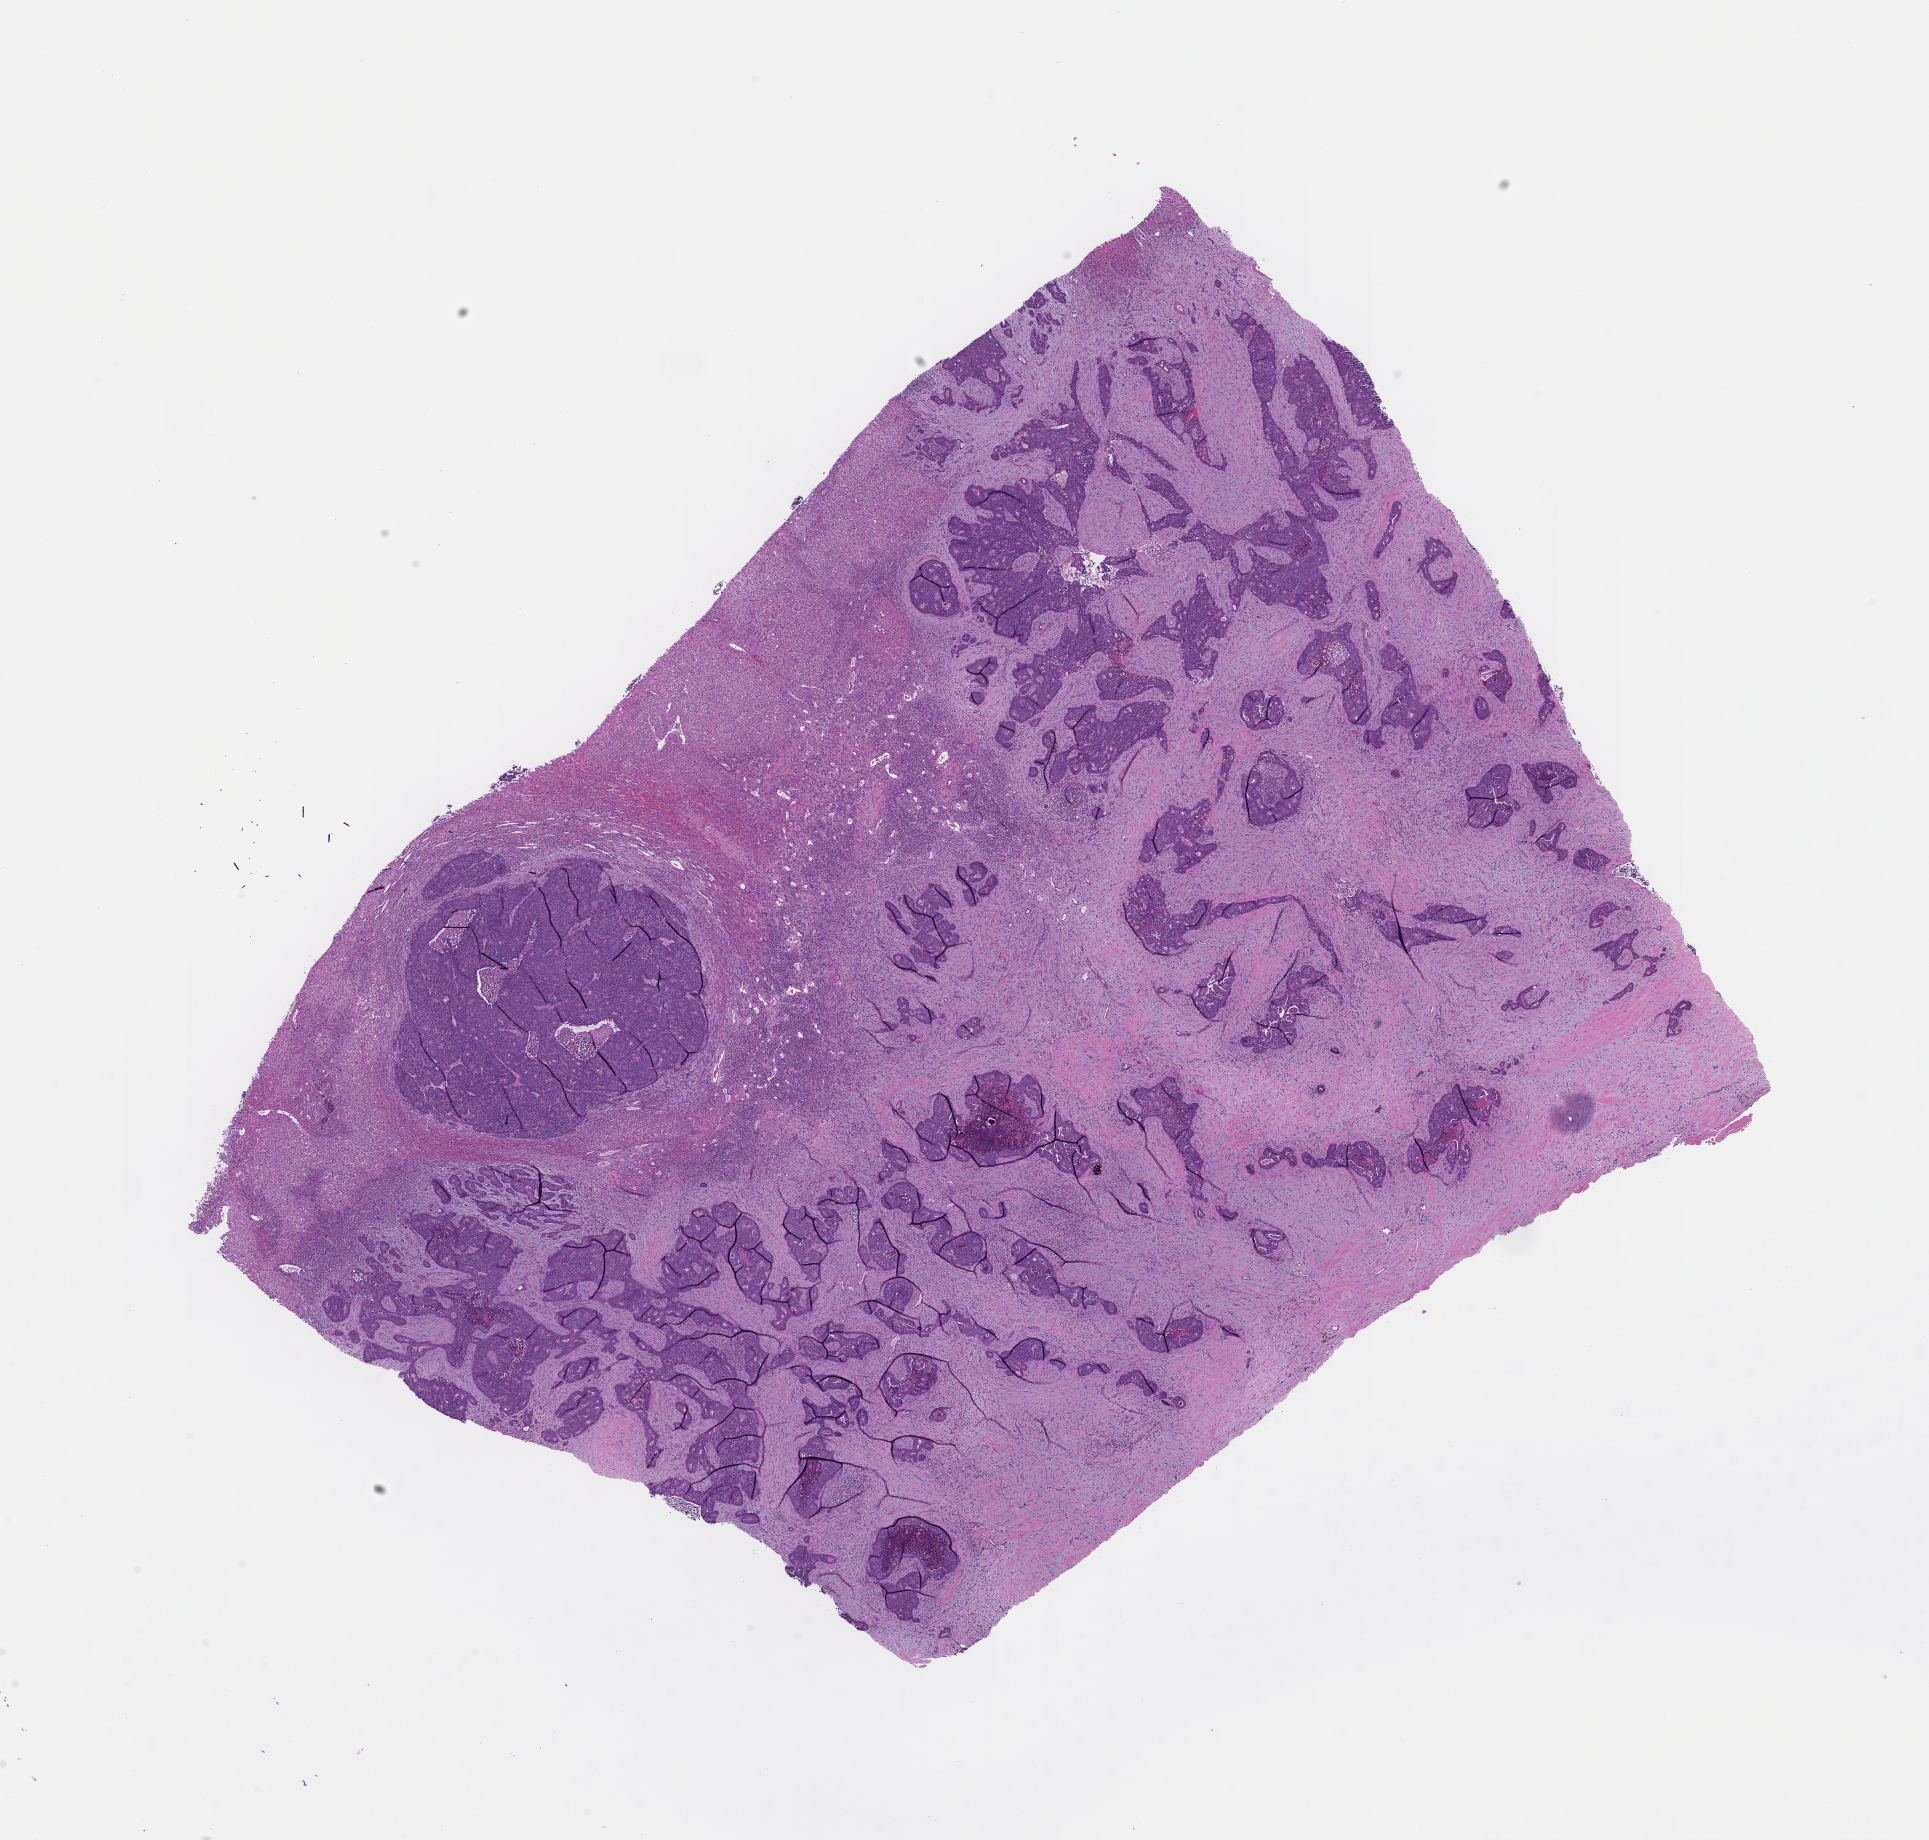
Whole-slide image, hematoxylin and eosin (H&E) stain — whole scanned area (about 15.6 x 14.9 mm) shown as a low-resolution overview; FFPE section; specimen time point: collected on treatment. Patient: female.
This section: metastatic tumor tissue. Primary diagnosis of the patient: Colorectal Carcinoma.